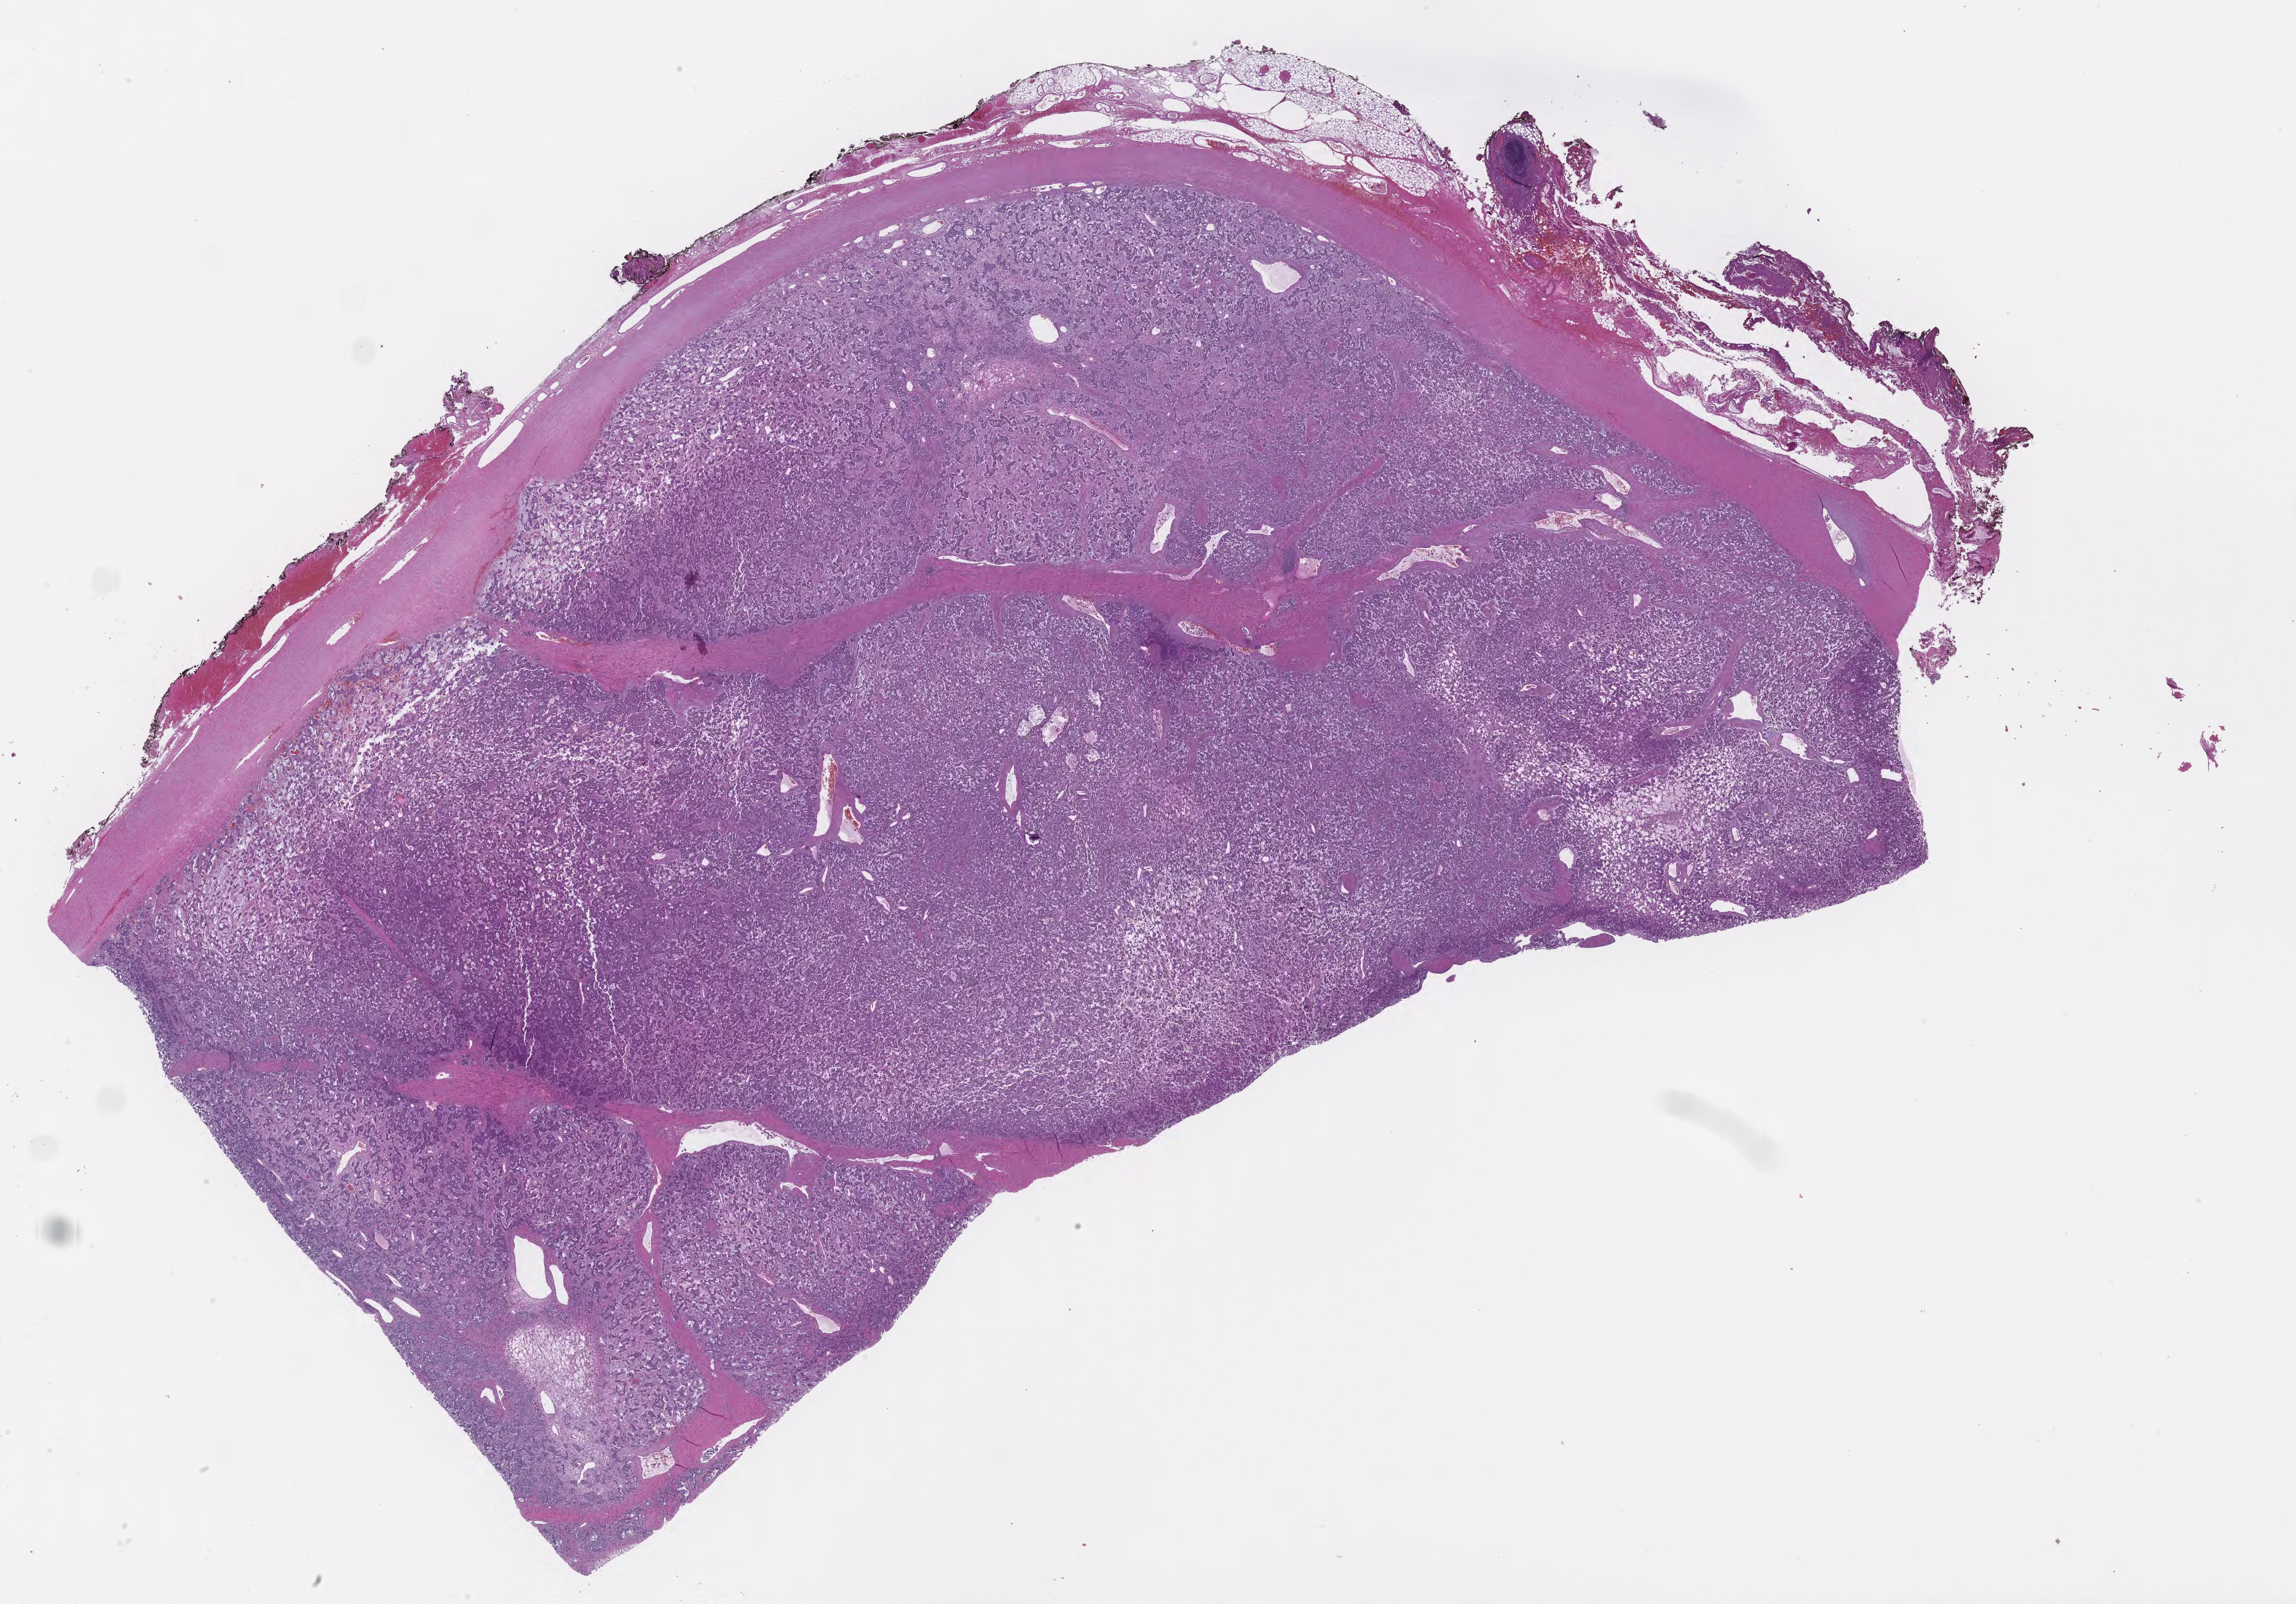
Whole-slide image, H&E stain of tumor tissue from the adrenal gland, whole scanned area (about 30.2 x 21.1 mm) shown as a low-resolution overview, formalin-fixed, paraffin-embedded (FFPE) tissue. Patient female; age 47 months (3 years 11 months).
* recorded diagnosis: Adrenal cortical carcinoma